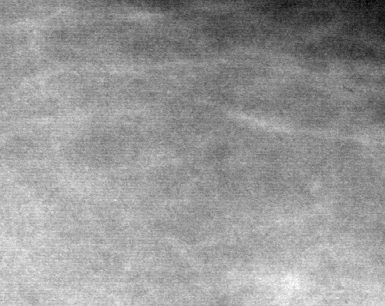
Cropped region of a digitized screen-film mammogram centred on a radiologist-marked abnormality; left breast; CC view.
Finding: calcifications, morphology pleomorphic, distribution clustered; BI-RADS assessment category 4; subtlety rating 4 on a 1 (subtle) to 5 (obvious) scale; pathology (as recorded): benign.